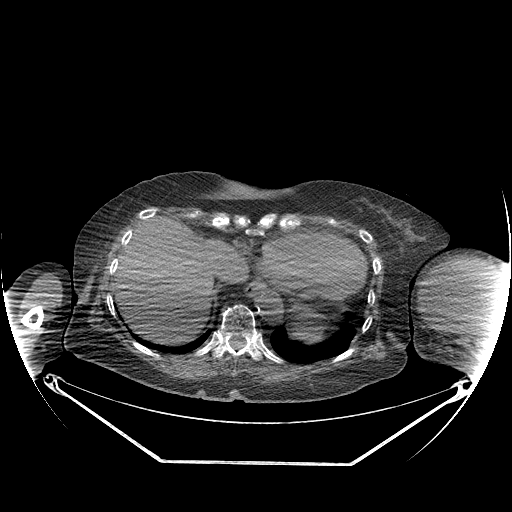
CT of an extremity soft-tissue mass (from a PET/CT study), one axial slice. Slice 145 of 267 in the series (ordered by position). Reconstruction kernel STANDARD. Soft-tissue window (W 400 / L 40 HU). 512 × 512 image matrix, field of view 500 × 500 mm. Female patient. From the clinical record (not read from this slice): histological type: pleiomorphic leiomyosarcoma; grade: high; site of the primary tumour: left biceps.
Outlined on this slice (expert contour drawn on MRI and transferred to this co-registered scan by the dataset authors):
- gross tumour volume including surrounding oedema: bounding box <425,260,499,321> (left, top, right, bottom; pixels)
- gross tumour volume (mass): <425,260,499,318>